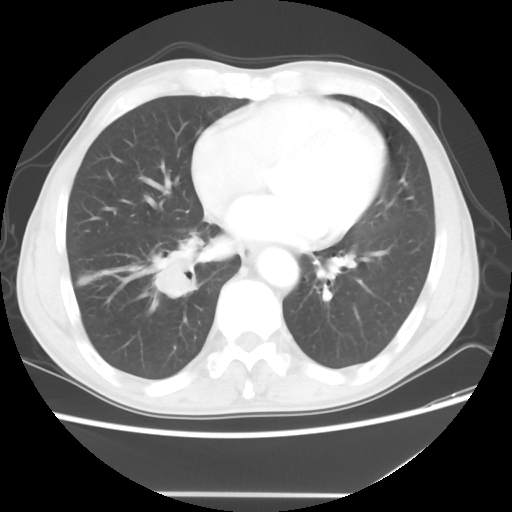
Chest CT, one axial slice. Slice 19 of 56 in the series (ordered by position). Lung window (W 1500 / L -600 HU). 5 mm slice thickness. 512 × 512 image matrix, field of view 344 × 344 mm. Patient: male, 65 years. Case-level facts recorded for this patient, not image findings: clinical TNM (as recorded): T1c N3 M0.
Outlined on this slice (rectangle marked by the reading radiologist):
- lung tumour (recorded histology: small cell carcinoma): bounding box (x1, y1, x2, y2) in pixels: (144, 253, 200, 299)